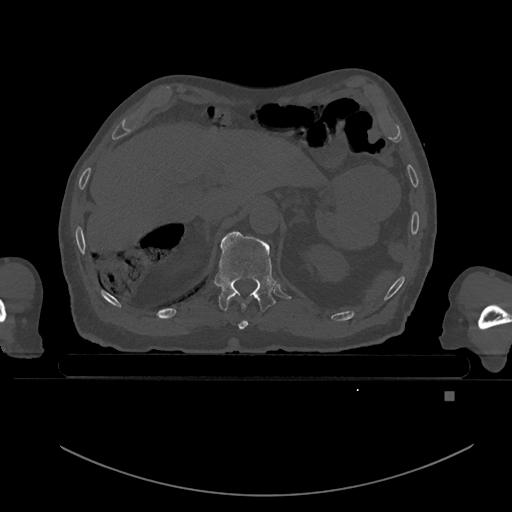
CT including the spine, one axial slice; position 41 of 969 along the scan axis; bone window (W 1800 / L 400 HU); 512 × 512 image matrix, field of view 456 × 456 mm. Male patient, age 82 years. From the clinical record (not read from this slice): primary cancer: prostate.
Annotated regions visible in this slice (semi-automatically segmented with operator editing):
- T10 vertebra: box from (x=238, y=320) to (x=248, y=329) px
- T11 vertebra: (x=215, y=231)–(x=277, y=313)